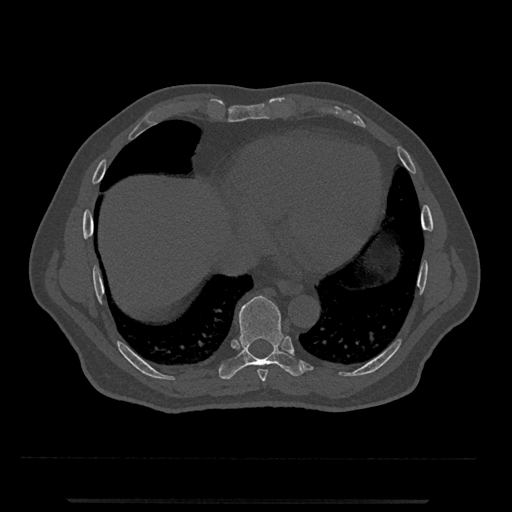
CT including the spine, one axial slice. Slice 586 of 797 in the series (ordered by position). 120 kVp. Bone window (W 1800 / L 400 HU). 0.5 mm slice thickness. 512 × 512 image matrix, field of view 419 × 419 mm. Patient: male, 63 years. From the clinical record (not read from this slice): primary cancer: prostate.
Structures marked on this image (semi-automatically segmented with operator editing):
- T8 vertebra: bounding box [x1, y1, x2, y2] px = [257, 369, 268, 382]
- T9 vertebra: [219, 296, 307, 380]